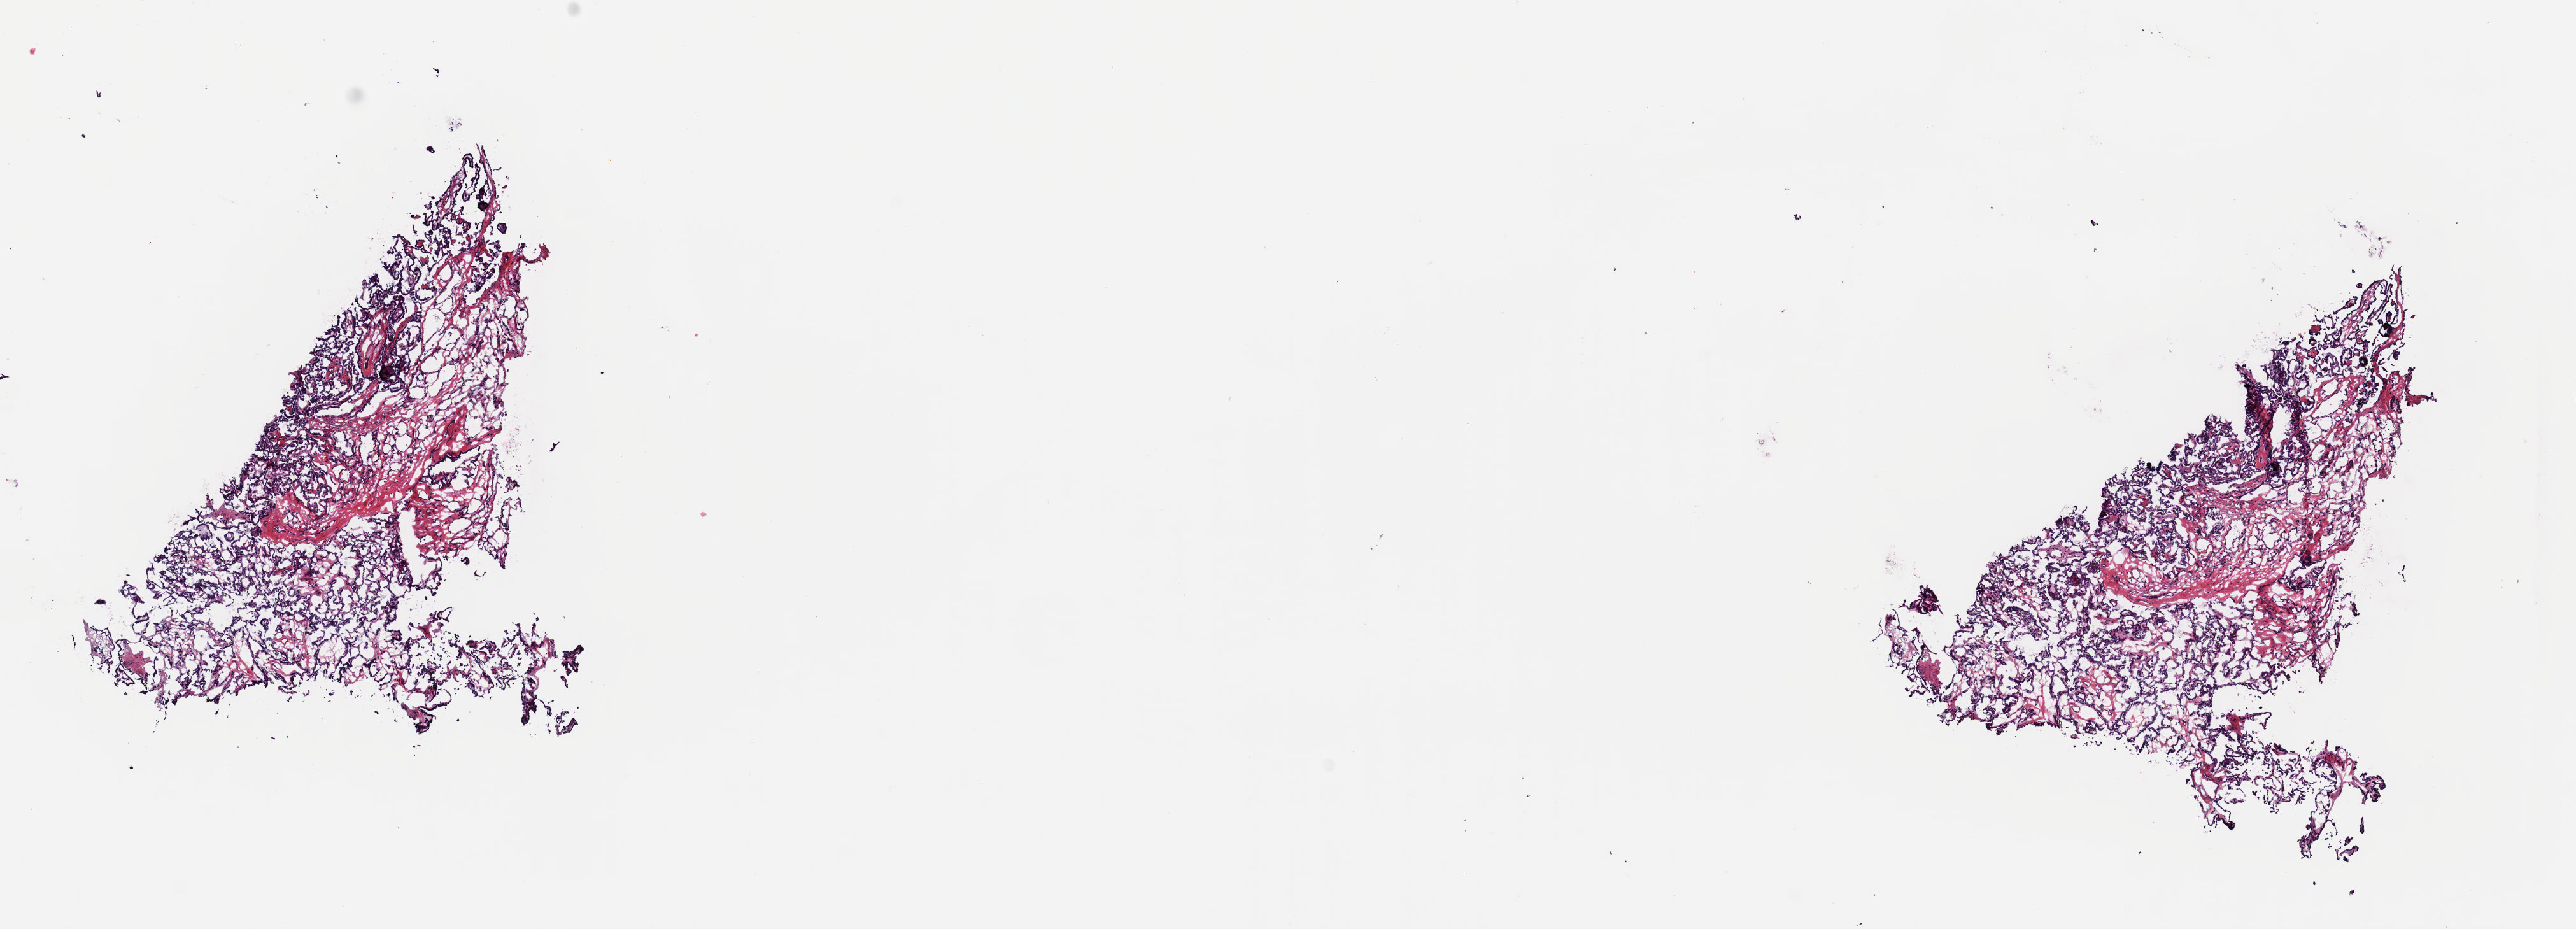
Digitized H&E tissue section (whole slide), shown as a low-resolution overview of the whole scanned area (about 16.0 x 5.8 mm, acquisition: 40x scan), frozen section from the top of the tissue portion, thyroid, primary tumour sample. Female patient; age at initial diagnosis 42 years. Pathologist review of this section (percent, as recorded): tumour cells 98%, tumour nuclei 90%, normal cells 0%, stromal cells 2%, necrosis 0%. Infiltration values recorded for this section: lymphocyte infiltration 0%, monocyte infiltration 0%, neutrophil infiltration 0%.
Lymph nodes positive (case pathology): 5 of 6 examined. Laterality: left. AJCC pathologic stage: I. Pathologic diagnosis: Papillary adenocarcinoma, NOS (thyroid gland).